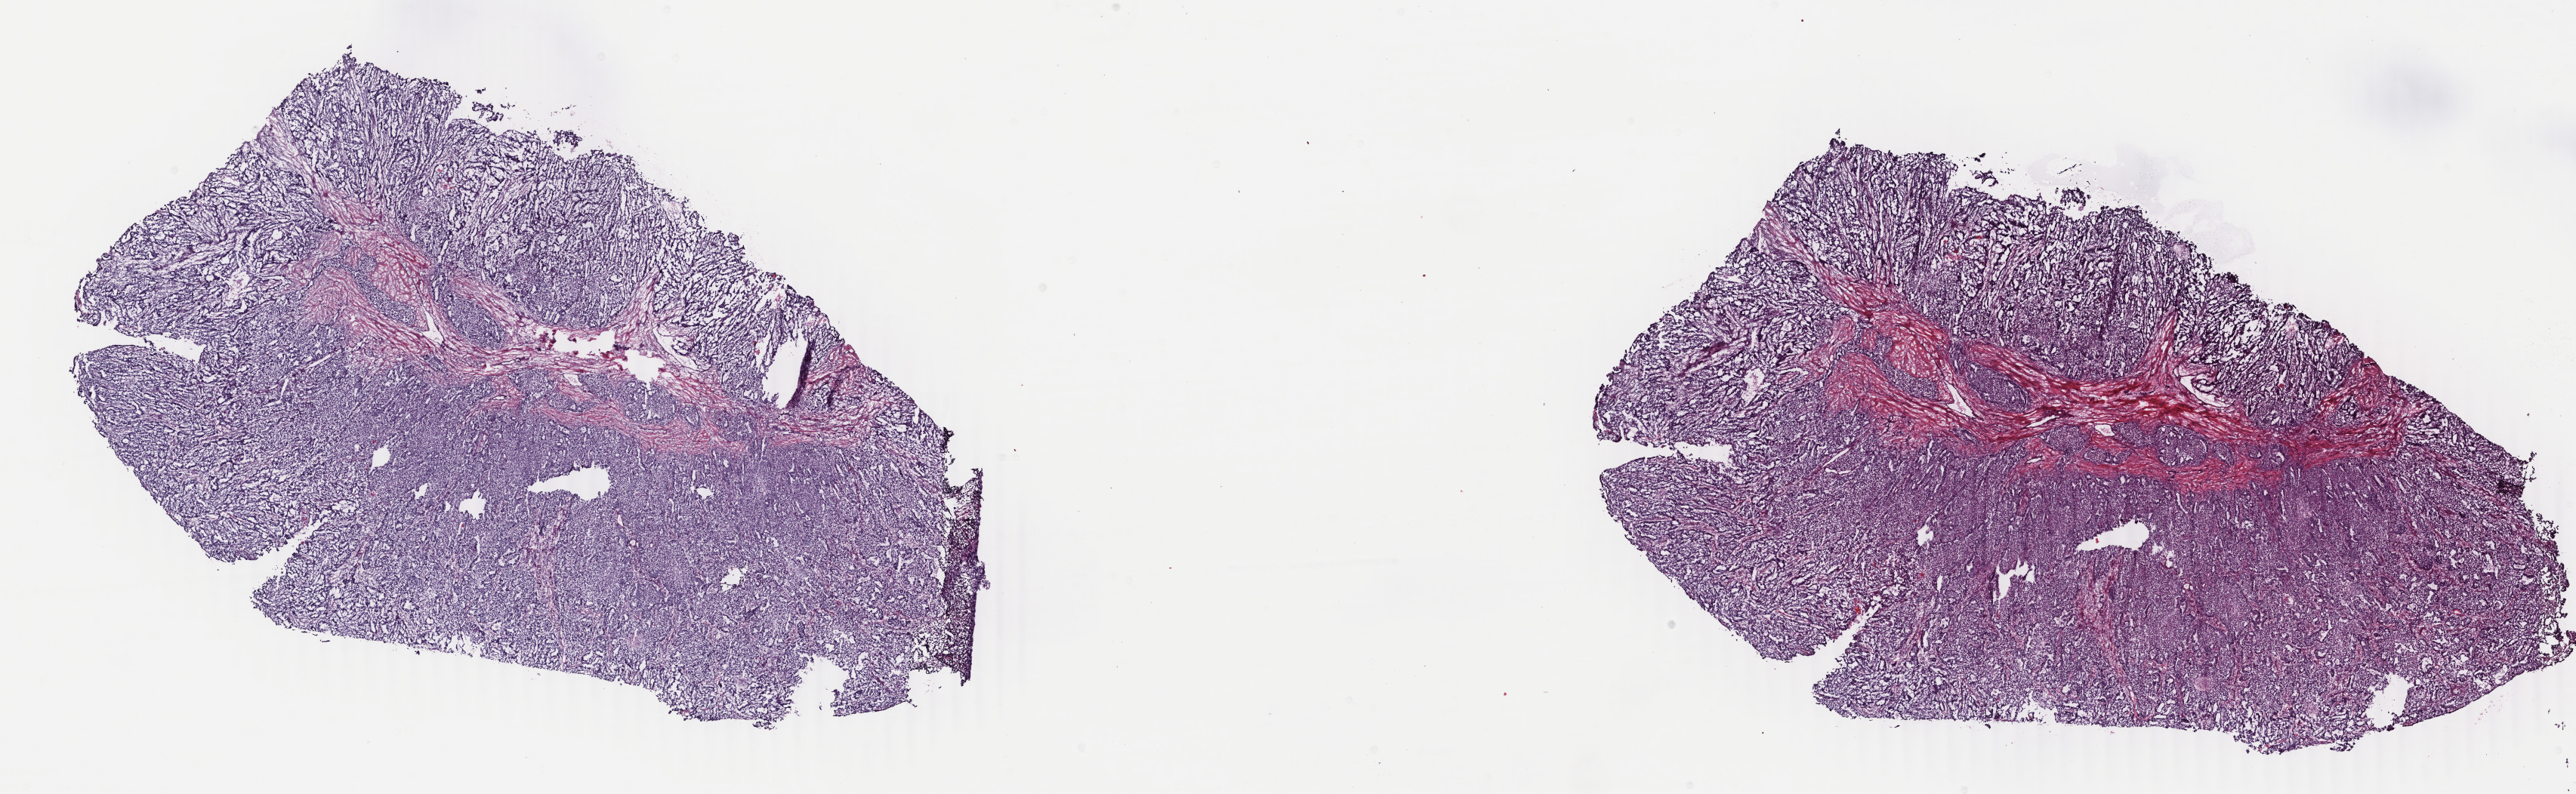
H&E-stained whole-slide image — low-resolution overview of the scanned area, about 27.1 x 8.4 mm, frozen section from the top of the tissue portion, sample: primary tumour, uterus. Patient: female, age at initial diagnosis 48 years. Histologic grade: G1 (well differentiated).
FIGO stage: IA. Pathologic diagnosis: Endometrioid adenocarcinoma, NOS (endometrium).